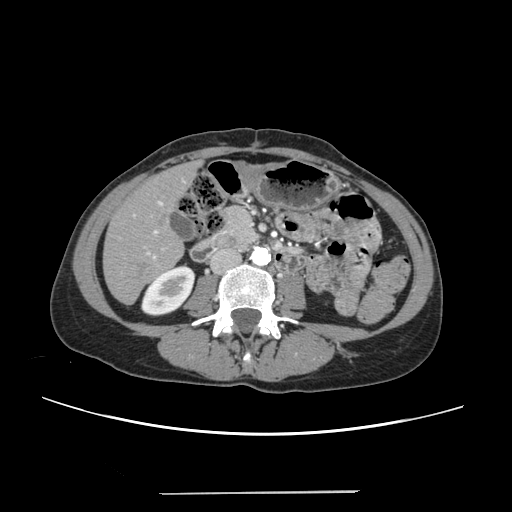
Contrast-enhanced abdominal CT, one axial slice; position 78 of 240 along the scan axis; 120 kVp; intravenous contrast given; soft-tissue window (W 400 / L 40 HU); 512 × 512 image matrix. Female patient, age 60 years. From the clinical record (not read from this slice): diagnosis: colorectal cancer liver metastases, imaged before liver resection; multiple liver metastases: no; largest metastasis: 1.5 cm; chemotherapy before resection: yes.
Outlined on this slice (manually delineated by an expert):
- liver: bounding box <105,164,196,303> (left, top, right, bottom; pixels)
- planned liver remnant (the part of the liver to remain after resection): <105,172,182,303>
- portal vein (with intrahepatic branches): <133,202,164,259>